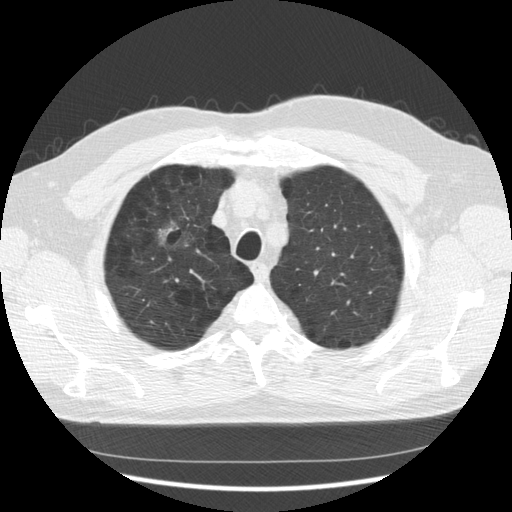
Low-dose screening chest CT, one axial slice. Slice 102 of 133 in the series (ordered by position). Reconstruction kernel STANDARD. 140 kVp. Lung window (W 1500 / L -600 HU). 512 × 512 image matrix, field of view 369 × 369 mm.
Outlined on this slice (outlined manually by an expert reader):
- lesion 1 (tumor, upper lobe of right lung): box from (x=158, y=222) to (x=178, y=244) px